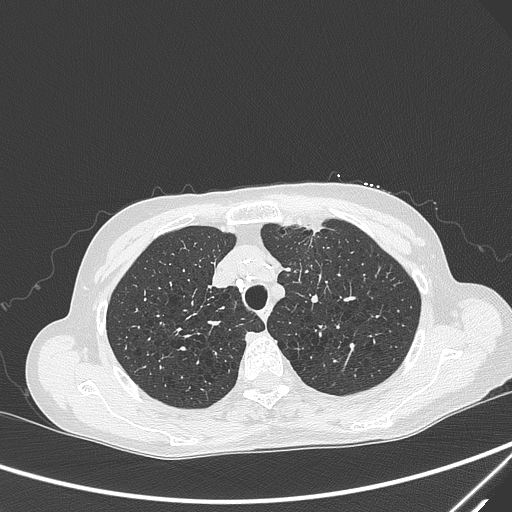
Chest CT, one axial slice; slice 238 of 299 in the series (ordered by position); 120 kVp; lung window (W 1500 / L -600 HU); 1 mm slice thickness; 512 × 512 image matrix, field of view 350 × 350 mm. Patient: female, 71 years. From the clinical record (not read from this slice): clinical TNM (as recorded): T1c N0 M0; histopathological grade: G2-3.
Annotated regions visible in this slice (rectangle marked by the reading radiologist):
- lung tumour (recorded histology: adenocarcinoma): bounding box <299,215,328,243> (left, top, right, bottom; pixels)